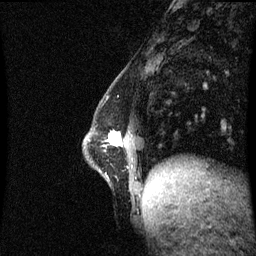
Breast MRI (dynamic contrast-enhanced), one sagittal slice. Slice 21 of 60 in the series (ordered by position). Dynamic contrast-enhanced series, image 2 of 3 at this slice position (ordered by acquisition). 1.5 T. TE 4.2 ms, TR 8.9 ms. 256 × 256 image matrix, field of view 210 × 210 mm. Patient: female, 47 years. Case-level facts recorded for this patient, not image findings: setting: breast cancer imaged before/during neoadjuvant chemotherapy; receptor status: HR-positive, HER2-negative.
Annotated regions visible in this slice (semi-automatic segmentation, software-assisted and operator-edited):
- analysis volume of interest (the breast-tissue region the enhancement analysis was run in; not a lesion): bounding box [x1, y1, x2, y2] px = [84, 132, 141, 194]
- tumour enhancement mask (voxels above the 70 % enhancement threshold inside the analysis volume of interest): [110, 133, 121, 146]